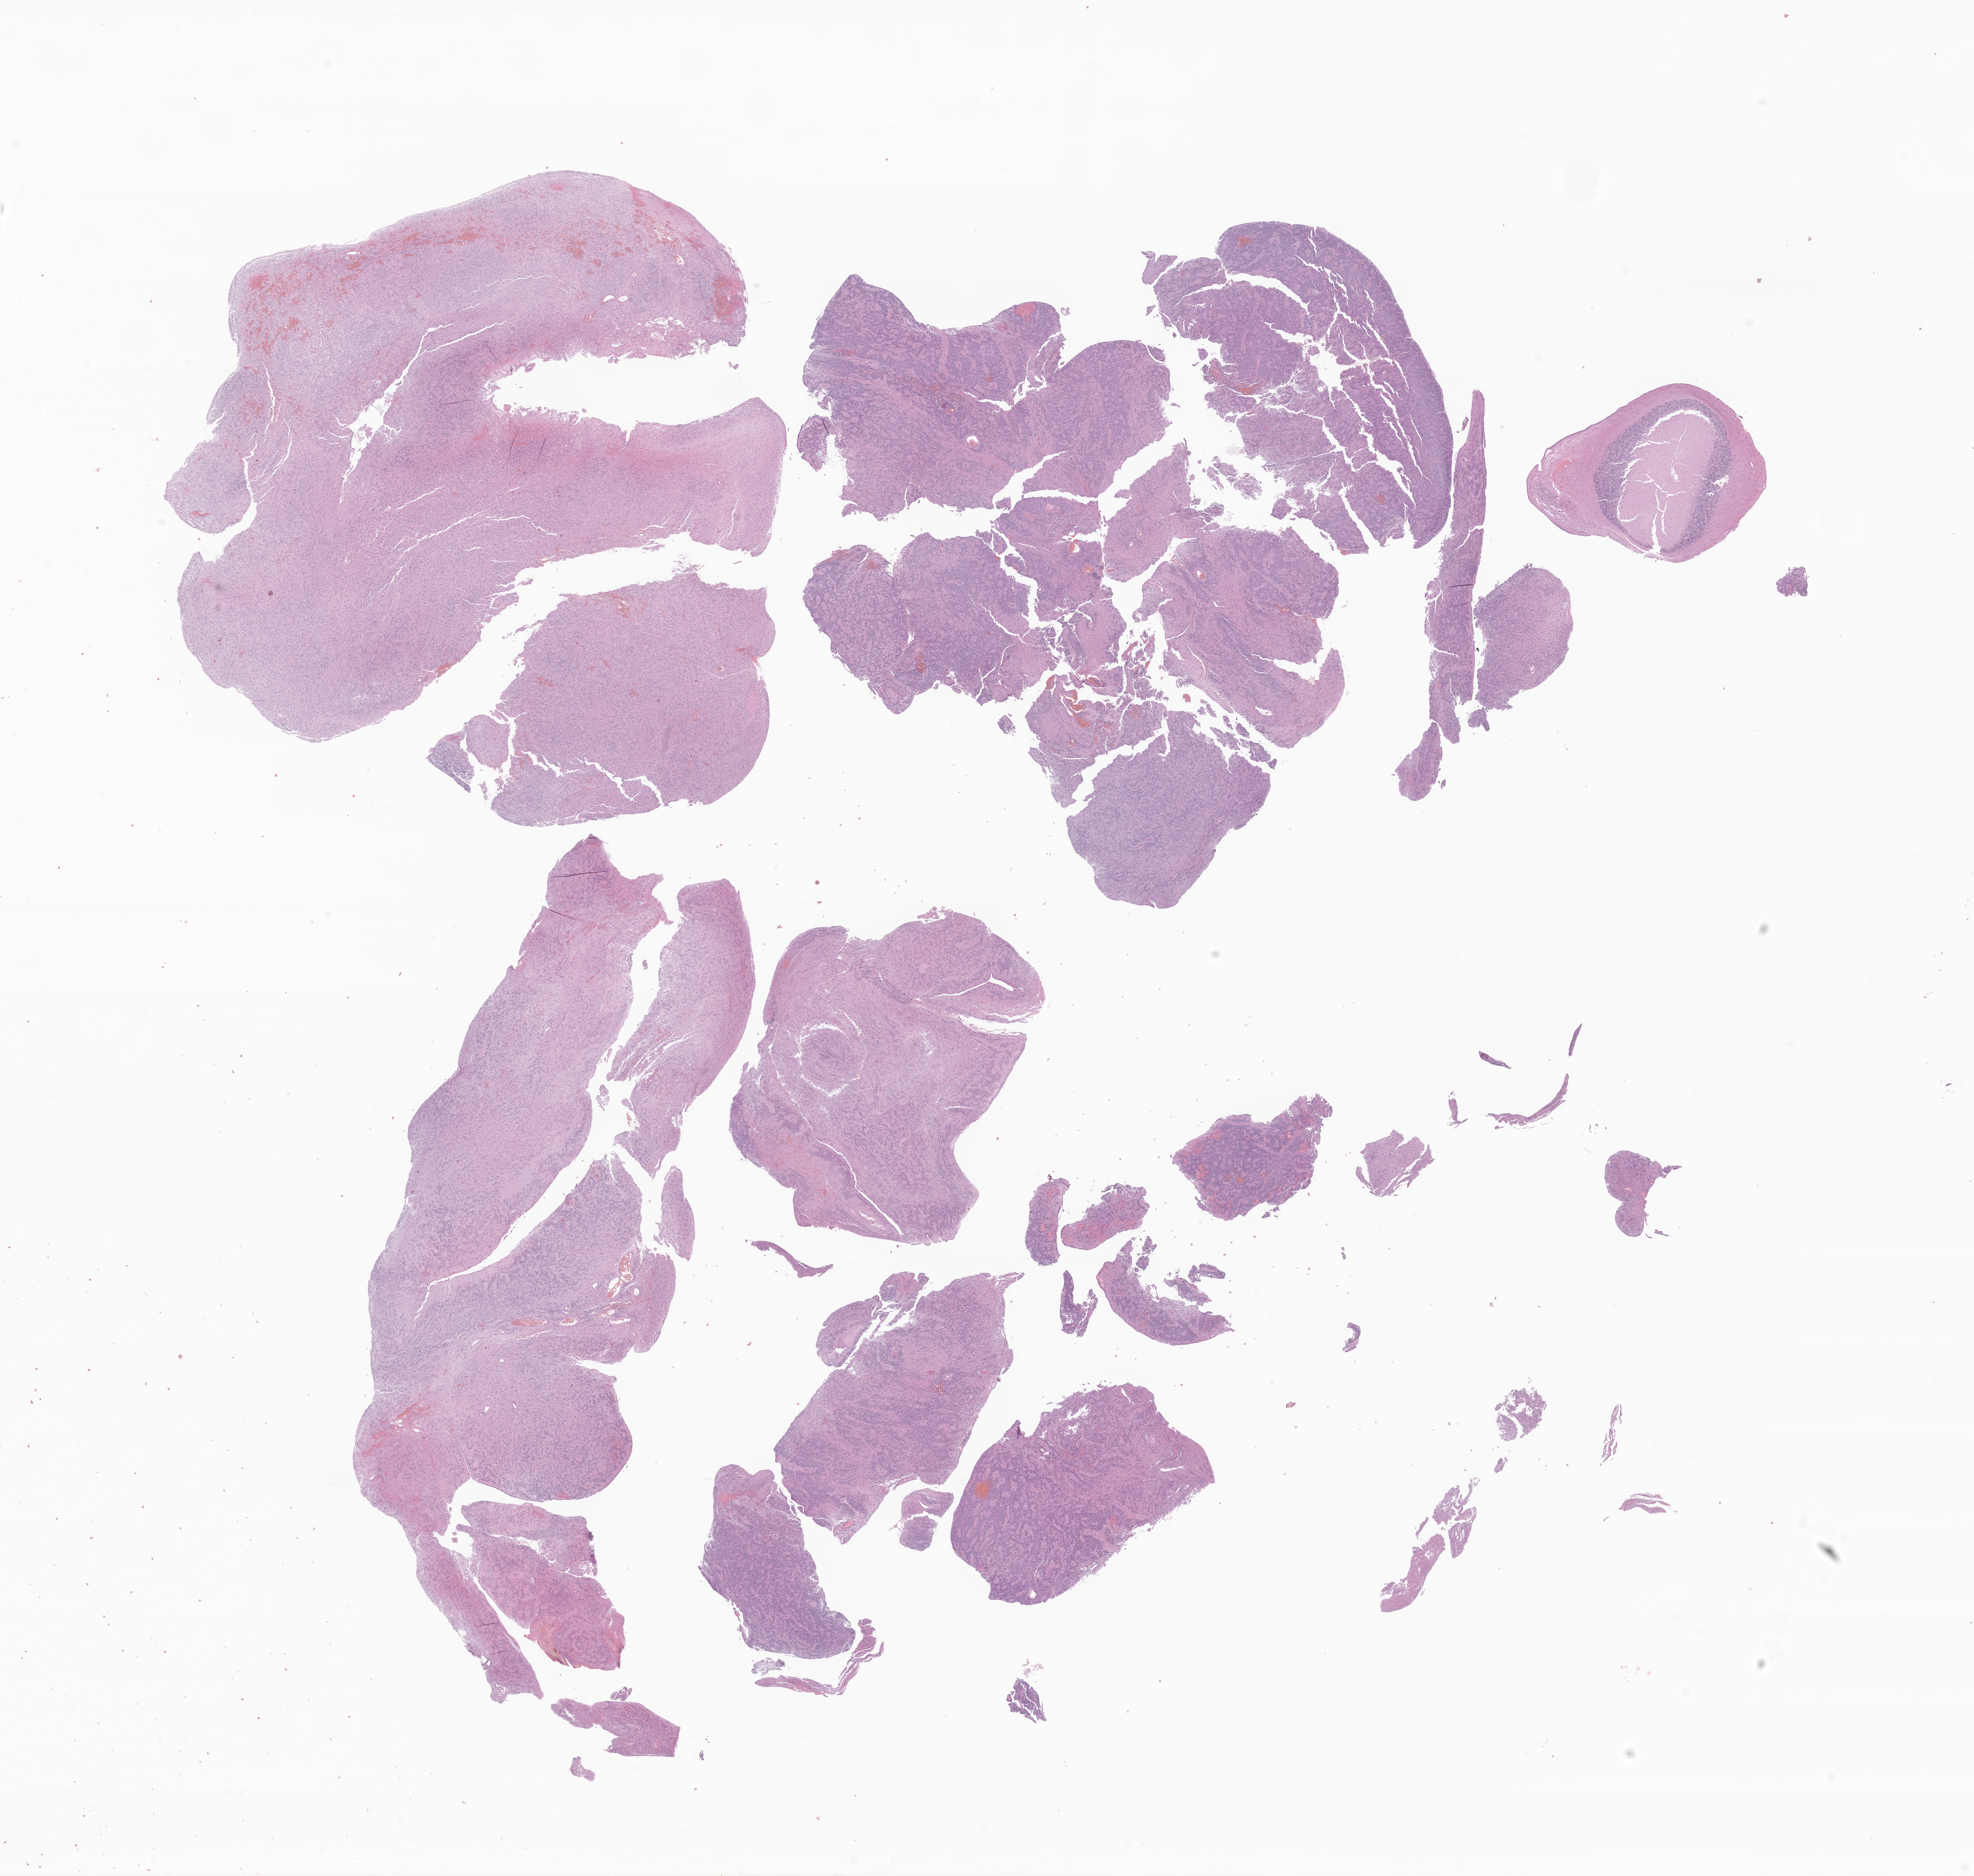
Hematoxylin and eosin (H&E) whole-slide image of tumor tissue from the brain — shown as a low-resolution overview of the whole scanned area (about 23.8 x 22.6 mm). Formalin-fixed paraffin-embedded section. Patient male; age 565 days (about 1.5 years).
Diagnosis (ICD-O-3 morphology term): Ependymoma, NOS.